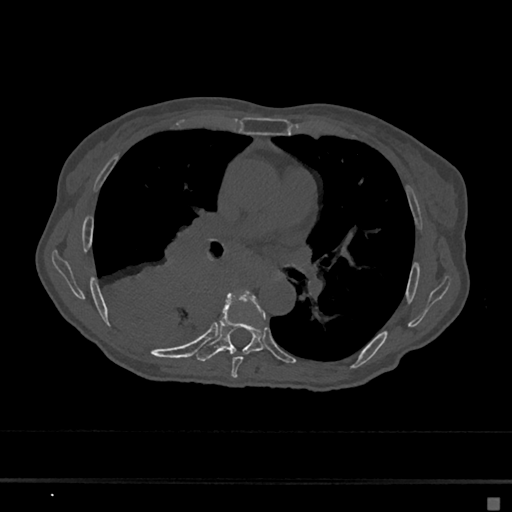
CT including the spine, one axial slice. Position 392 of 797 along the scan axis. Bone window (W 1800 / L 400 HU). 0.5 mm slice thickness. 512 × 512 image matrix, field of view 360 × 360 mm. Patient: female, 68 years. From the clinical record (not read from this slice): primary cancer: renal.
Annotated regions visible in this slice (semi-automatic segmentation, software-assisted and operator-edited):
- T6 vertebra: bounding box (x1, y1, x2, y2) in pixels: (231, 291, 265, 379)
- T7 vertebra: (196, 293, 264, 361)